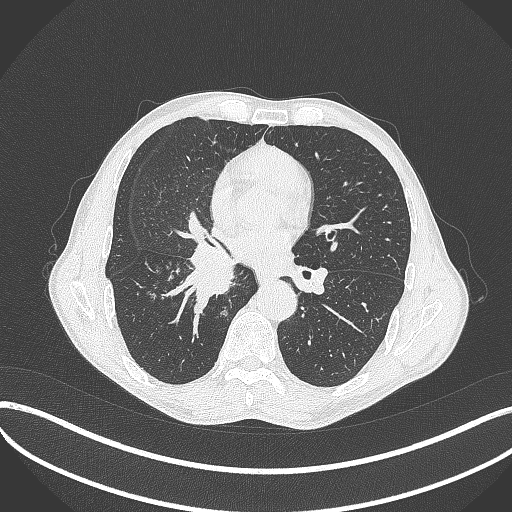
Chest CT, one axial slice; position 215 of 481 along the scan axis; reconstruction kernel B70f; lung window (W 1500 / L -600 HU); 512 × 512 image matrix, field of view 400 × 400 mm. Patient: male, 65 years. From the clinical record (not read from this slice): clinical TNM (as recorded): T2a N0 M0.
Structures marked on this image (rectangle marked by the reading radiologist):
- lung tumour (recorded histology: squamous cell carcinoma): box from (x=165, y=243) to (x=242, y=309) px